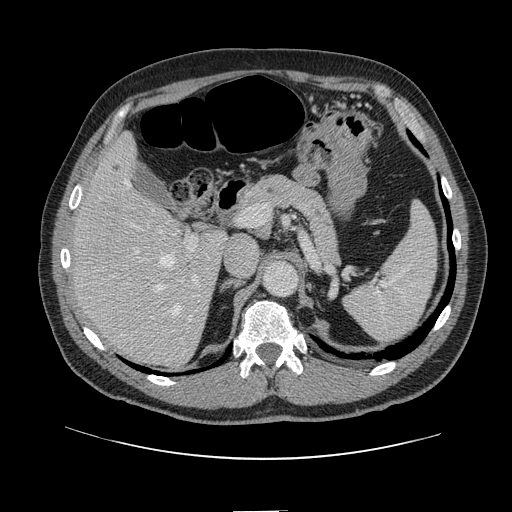
Contrast-enhanced abdominal CT, one axial slice; slice 83 of 161 in the series (ordered by position); 120 kVp; intravenous contrast given; soft-tissue window (W 400 / L 40 HU); 2.5 mm slice thickness; 512 × 512 image matrix. Male patient, age 66 years. From the clinical record (not read from this slice): diagnosis: colorectal cancer liver metastases, imaged before liver resection; multiple liver metastases: no; largest metastasis: 3.5 cm; disease in both lobes: no.
Annotated regions visible in this slice (manually delineated by an expert):
- hepatic veins: box from (x=100, y=179) to (x=183, y=314) px
- liver: (x=75, y=137)–(x=224, y=365)
- planned liver remnant (the part of the liver to remain after resection): (x=75, y=136)–(x=180, y=301)
- portal vein (with intrahepatic branches): (x=127, y=217)–(x=250, y=298)
- liver metastasis: (x=114, y=166)–(x=121, y=172)